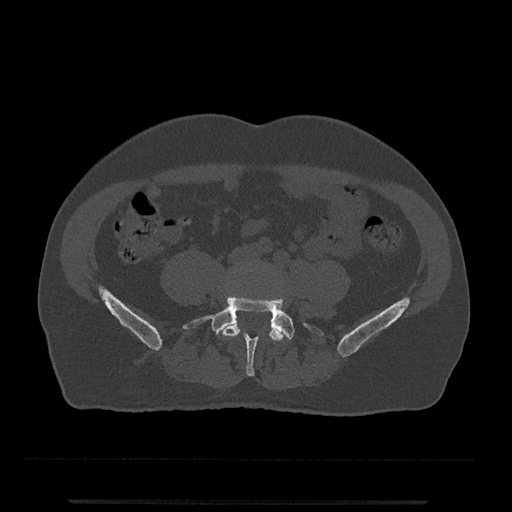
CT including the spine, one axial slice. Slice 92 of 797 in the series (ordered by position). Reconstruction kernel Br40s/3. 120 kVp. Bone window (W 1800 / L 400 HU). 0.5 mm slice thickness. 512 × 512 image matrix. Male patient, age 63 years. Case-level facts recorded for this patient, not image findings: primary cancer: prostate.
Structures marked on this image (semi-automatic segmentation, software-assisted and operator-edited):
- L4 vertebra: bounding box [x1, y1, x2, y2] px = [222, 319, 287, 344]
- L5 vertebra: [183, 296, 323, 376]